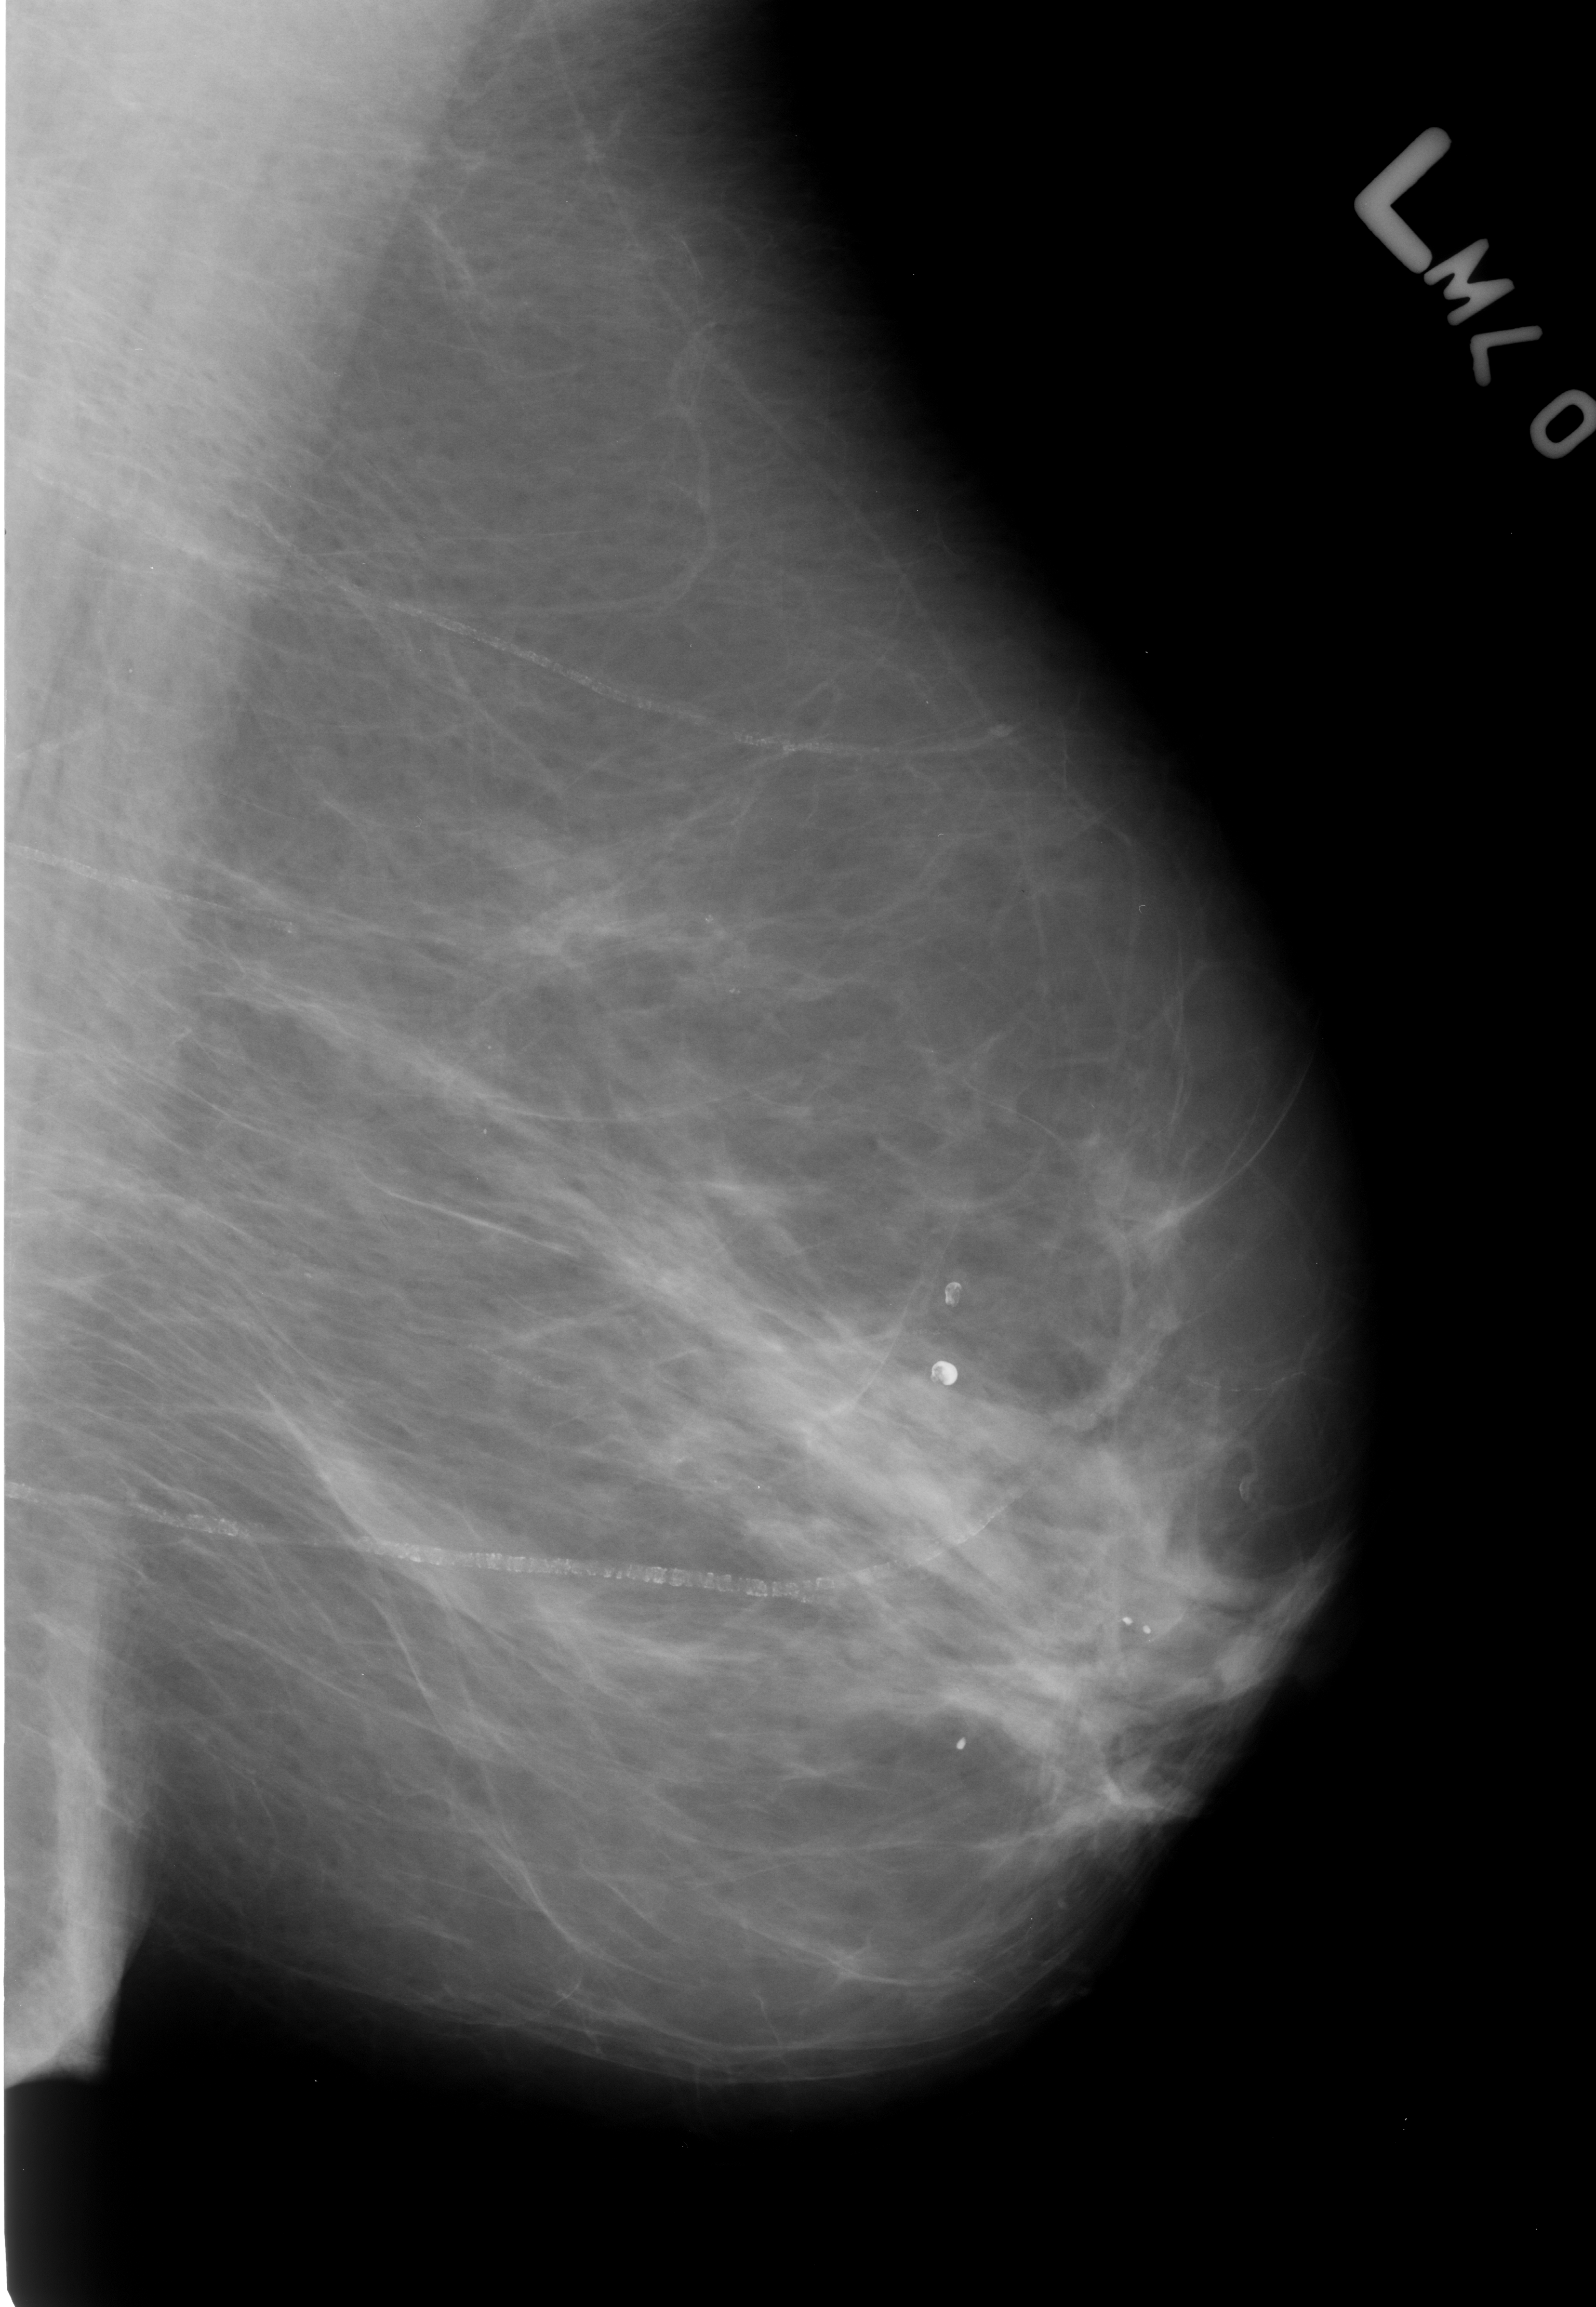
Digitized screen-film mammogram; left breast; MLO view; breast composition: scattered fibroglandular densities (BI-RADS density category 2 of 4).
- Marked findings (only marked abnormalities are described; nothing is implied about the rest of the image): Finding 1 of 4: calcifications, morphology vascular / coarse / lucent centered; BI-RADS assessment category 2; benign without callback (not worked up further).
- Finding 2 of 4: calcifications, morphology vascular / coarse / lucent centered; BI-RADS assessment category 2; benign; no additional work-up was recommended (benign without callback).
- Finding 3 of 4: calcifications, morphology vascular / coarse / lucent centered; BI-RADS assessment category 2; benign; no additional work-up was recommended (benign without callback).
- Finding 4 of 4: calcifications, morphology vascular / coarse / lucent centered; BI-RADS assessment category 2; benign; no additional work-up was recommended (benign without callback).